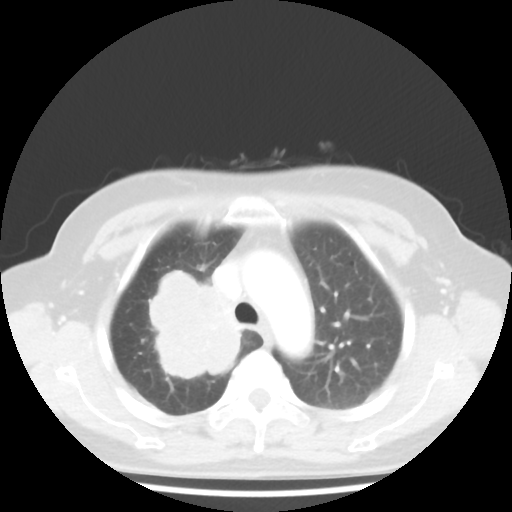
Chest CT, one axial slice; slice 33 of 44 in the series (ordered by position); reconstruction kernel STANDARD; 100 kVp; lung window (W 1500 / L -600 HU); 5 mm slice thickness; 512 × 512 image matrix, field of view 316 × 316 mm. Patient: female, 62 years. From the clinical record (not read from this slice): clinical TNM (as recorded): T3 N0 M0; histopathological grade: G3.
Annotated regions visible in this slice (bounding box drawn by a radiologist):
- lung tumour (recorded histology: small cell carcinoma): bounding box (x1, y1, x2, y2) in pixels: (137, 248, 254, 393)